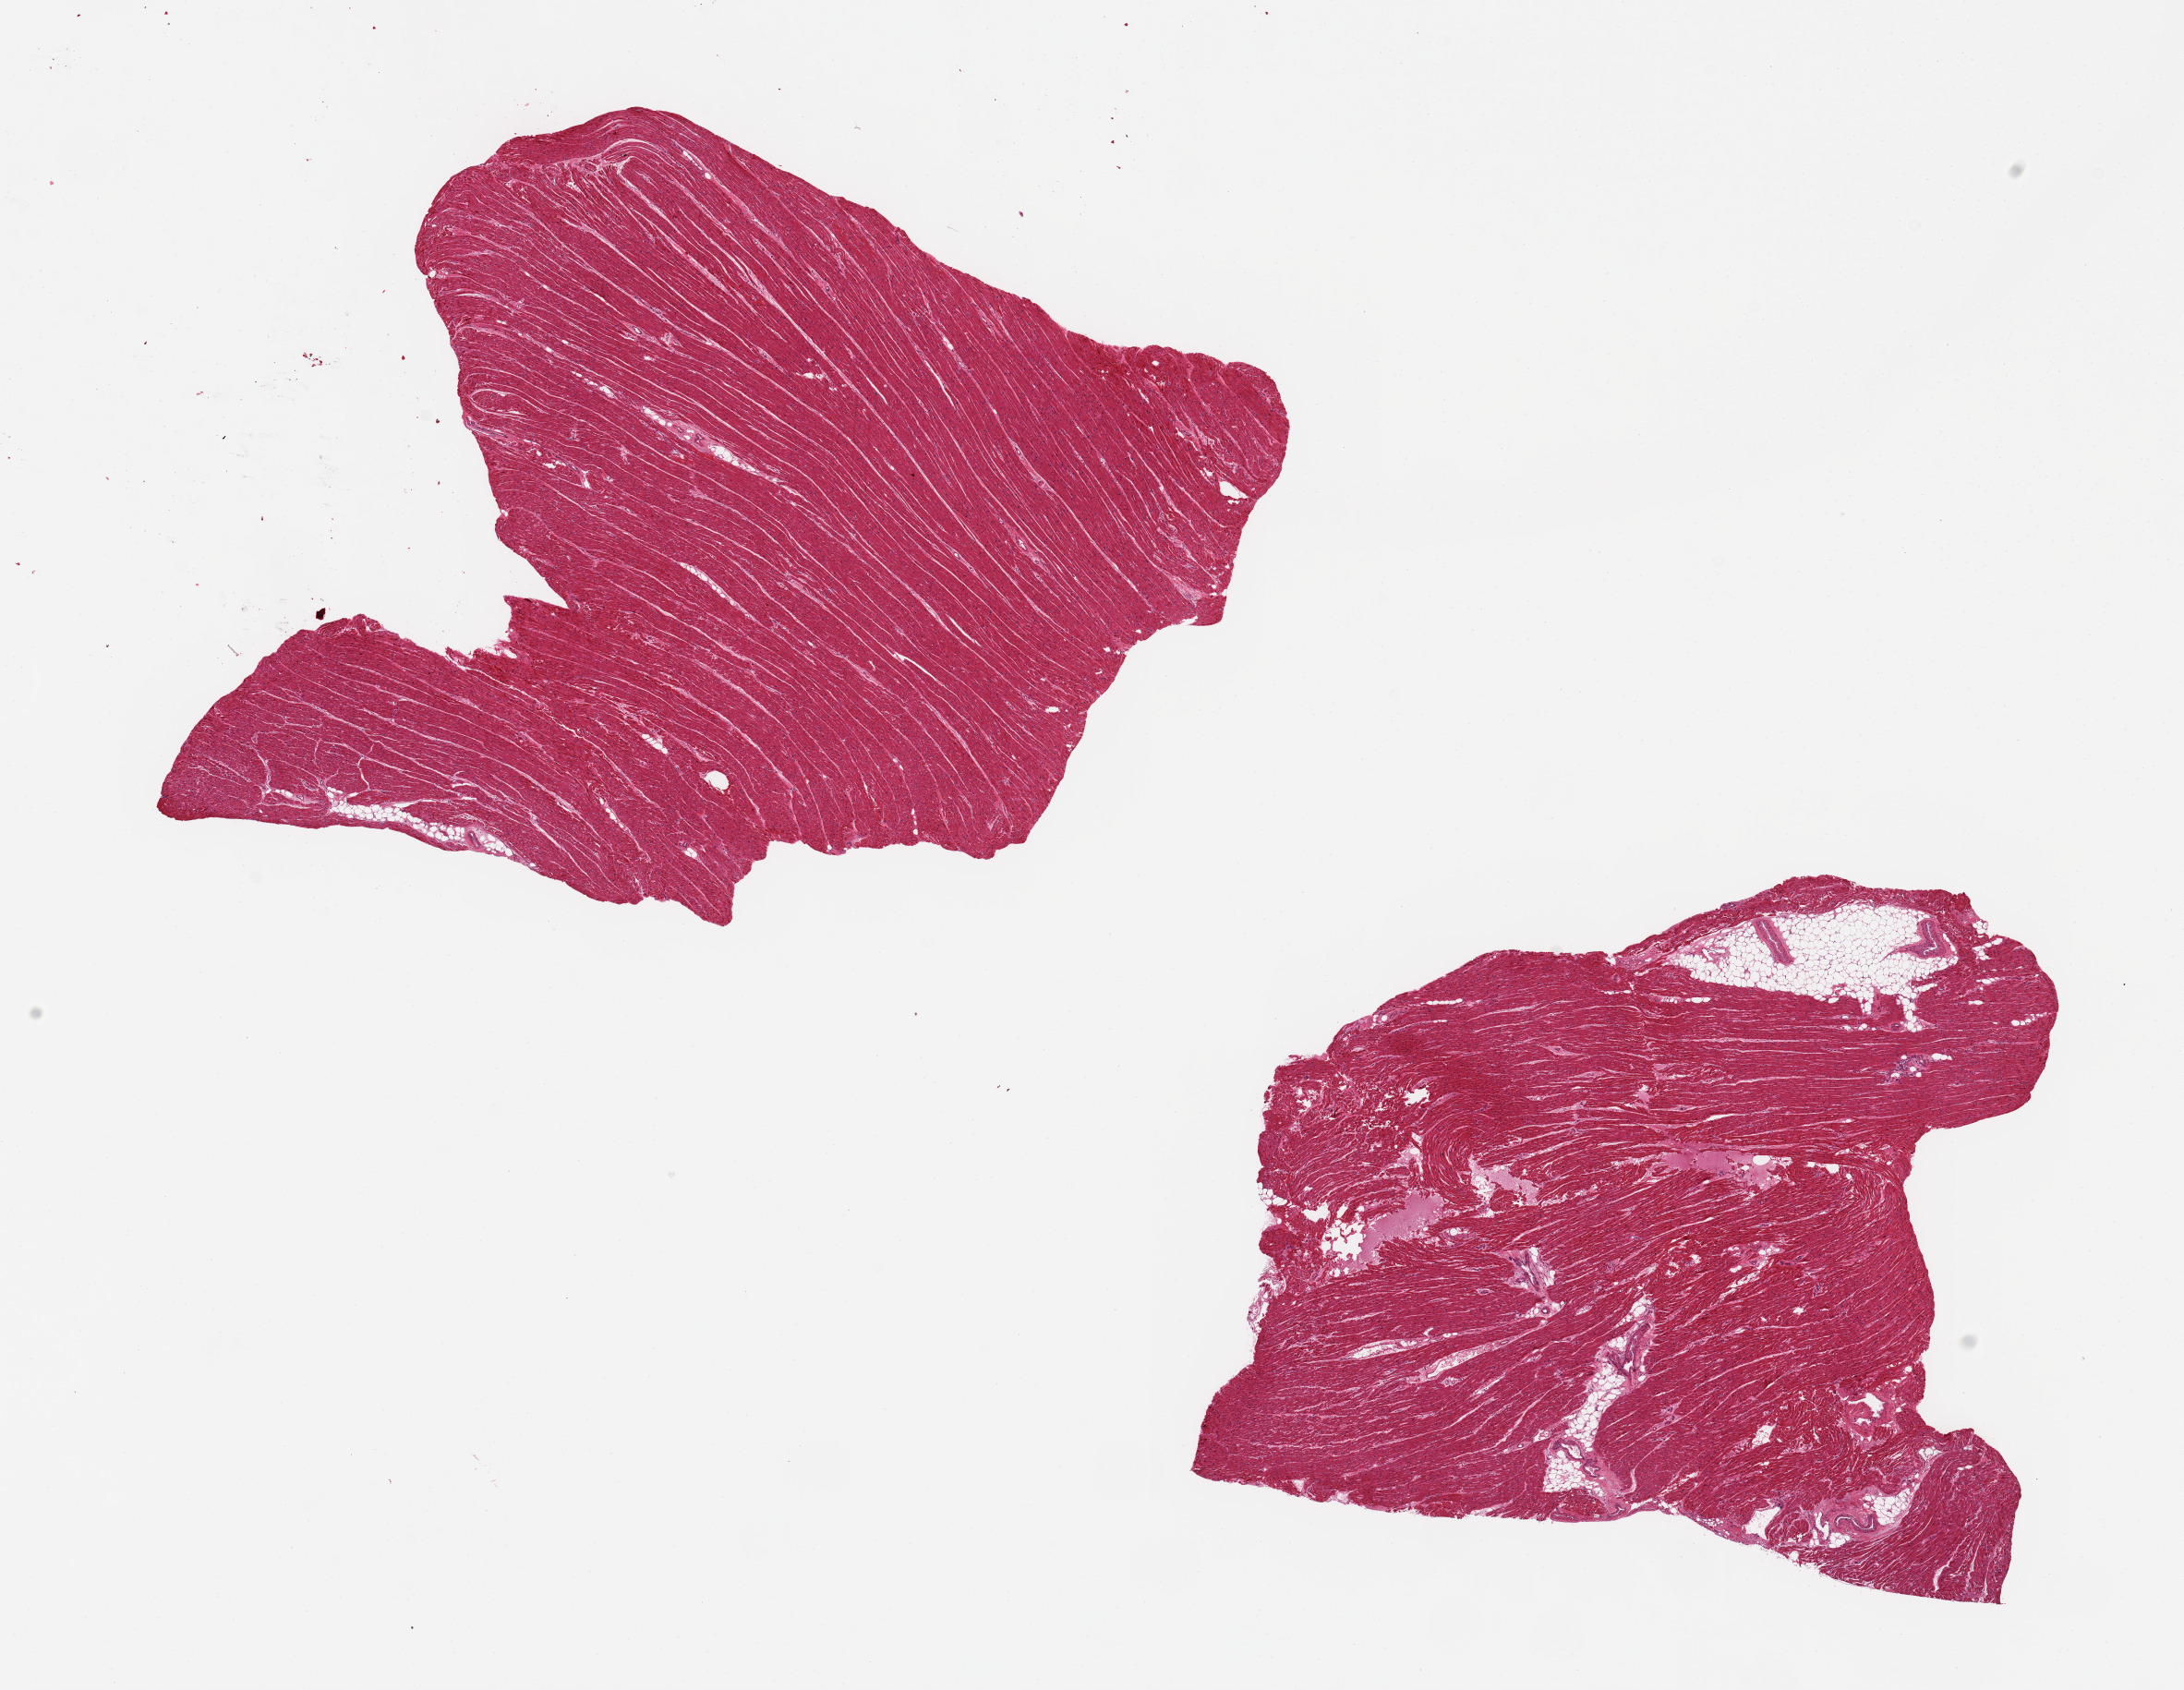
Hematoxylin and eosin (H&E) whole-slide image — whole scanned area (about 18.7 x 14.5 mm) shown as a low-resolution overview; PAXgene-fixed paraffin-embedded (PFPE) section; section of heart (target tissue); donor tissue sample. Donor sex: female.
Reviewer comment on this tissue sample: 2 ~7x6mm aliquots. Contraction band ischemic changes noted; focal fat in one aliquot.